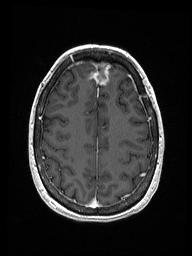
Brain MRI from a brain-tumour surgery series, one axial slice; position 49 of 192 along the scan axis; T1-weighted post-contrast; 1 mm slice thickness; 192 × 256 image matrix. From the clinical record (not read from this slice): histopathology: Metastastic Carcinoma from Breast primary; tumour location: Right Frontal.
Structures marked on this image (manually delineated by an expert):
- previous resection cavity: bounding box (x1, y1, x2, y2) in pixels: (93, 62, 111, 85)